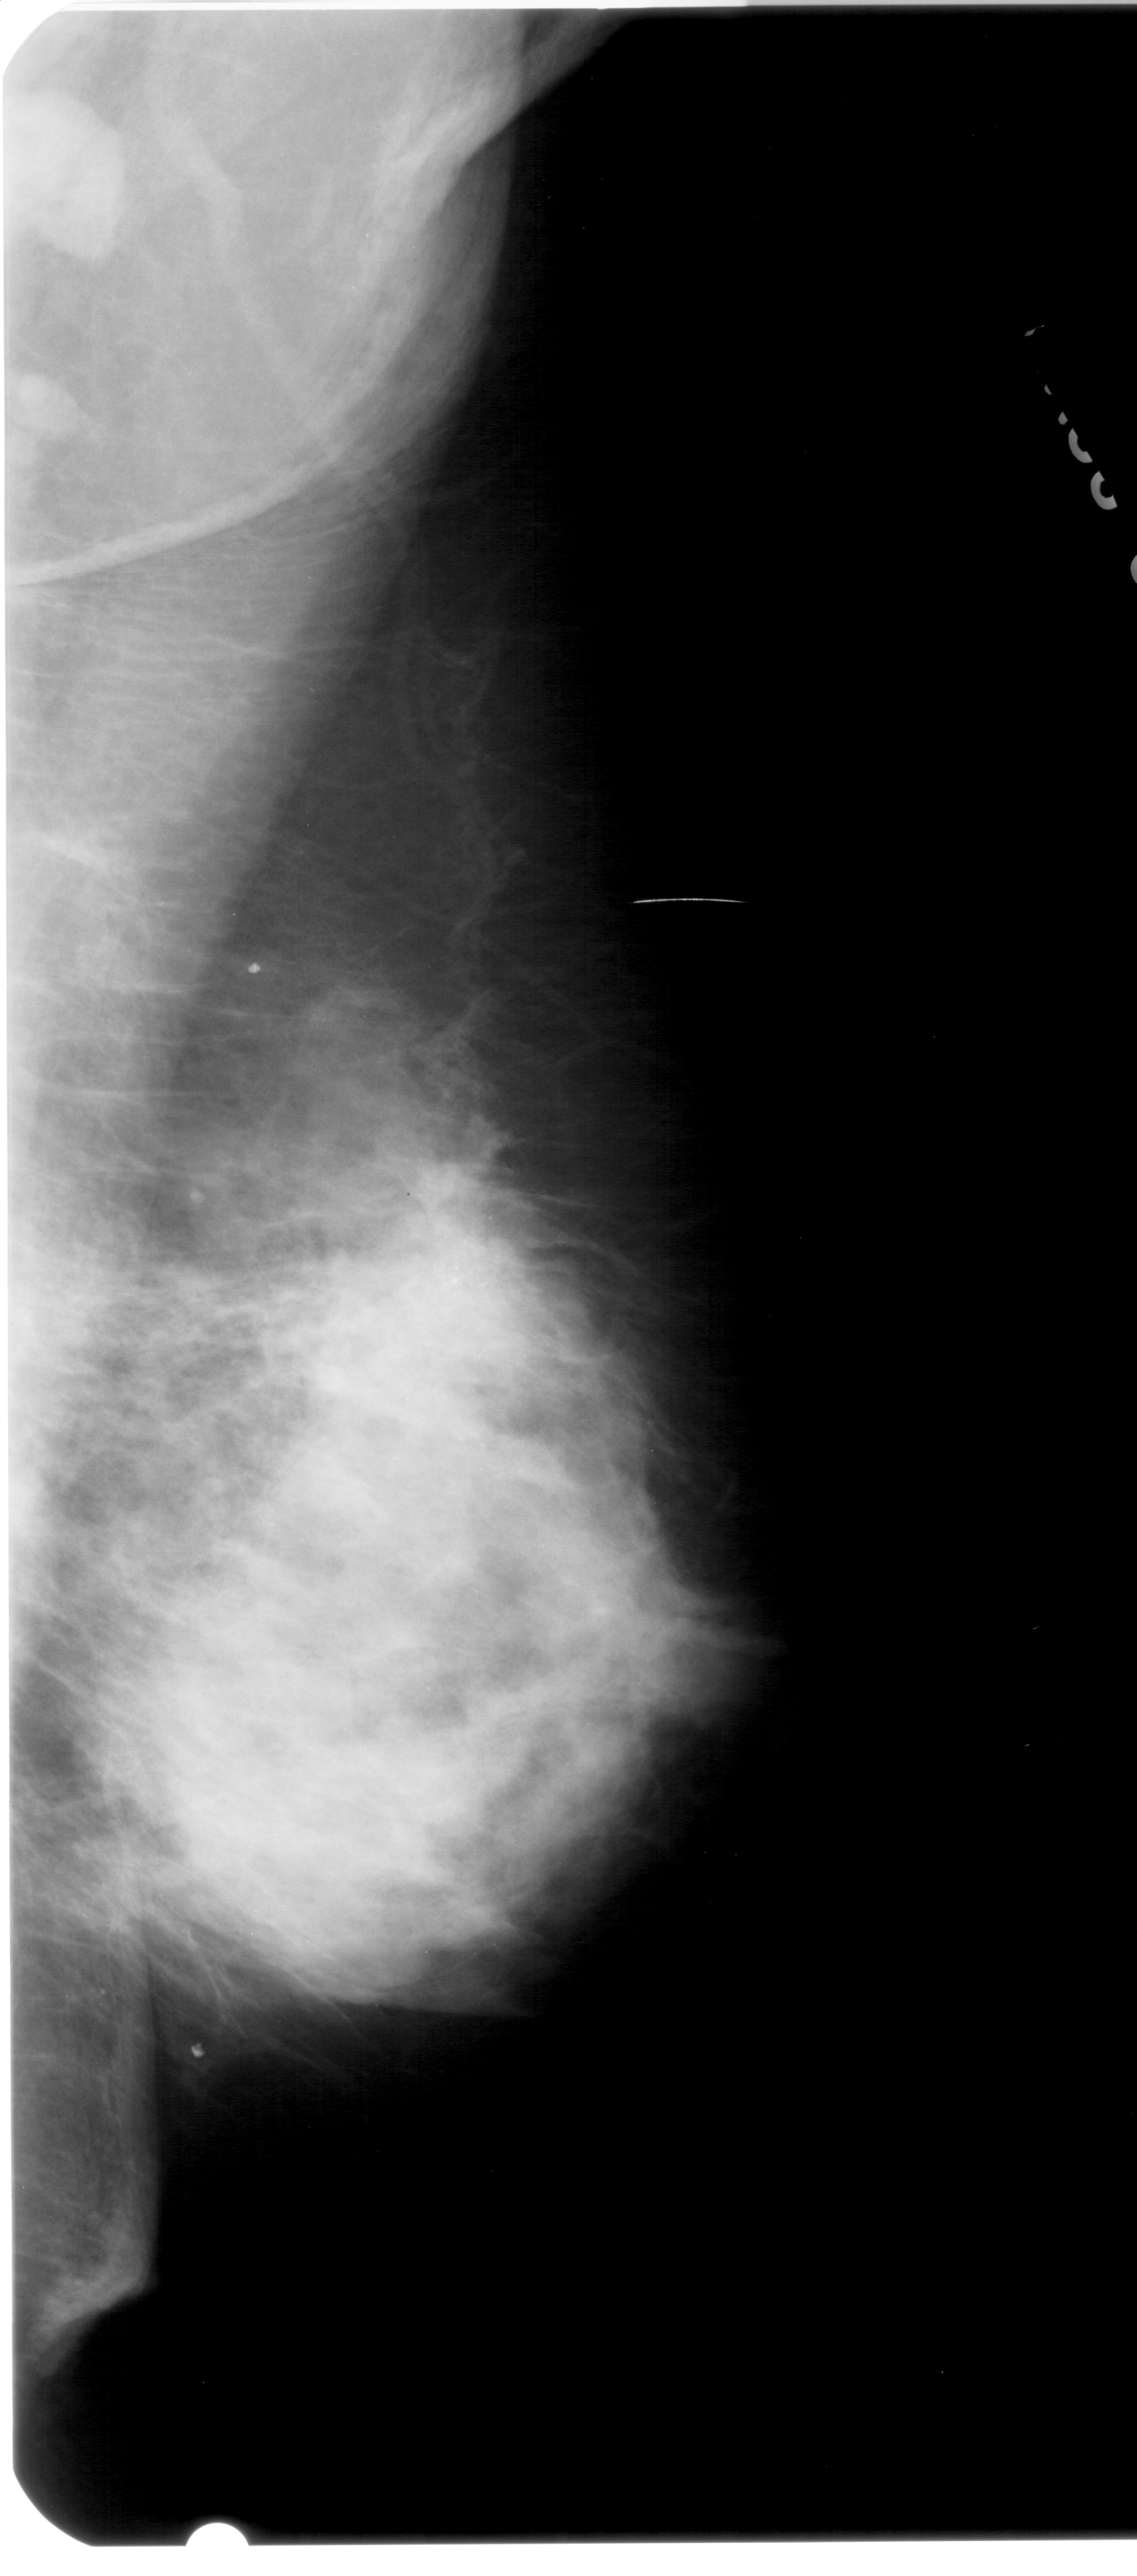
Scanned film-screen mammogram; right breast; MLO view; BI-RADS breast density category 3 (scale 1–4).
- Marked findings (only marked abnormalities are described; nothing is implied about the rest of the image): mass, shape architectural distortion, margins spiculated; BI-RADS assessment category 5; subtlety rating 5 on a 1 (subtle) to 5 (obvious) scale; pathology result (as recorded, not read from the image): malignant.